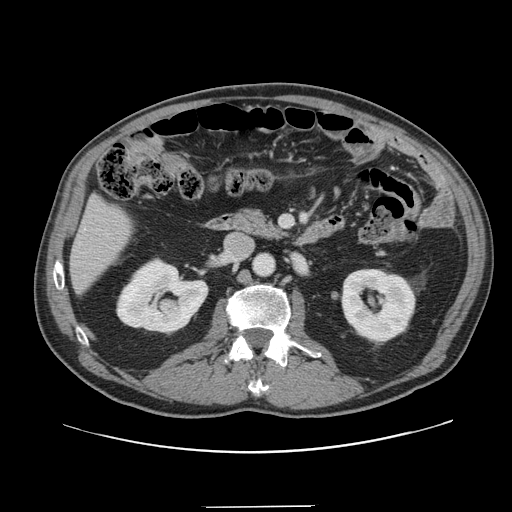
Contrast-enhanced abdominal CT, one axial slice; position 58 of 139 along the scan axis; 120 kVp; intravenous contrast given; soft-tissue window (W 400 / L 40 HU); 2.5 mm slice thickness; 512 × 512 image matrix, field of view 397 × 397 mm. Male patient, age 64 years. Case-level facts recorded for this patient, not image findings: diagnosis: colorectal cancer liver metastases, imaged before liver resection; multiple liver metastases: yes; largest metastasis: 3.5 cm; chemotherapy before resection: yes.
Outlined on this slice (manually delineated by an expert):
- liver: bounding box (x1, y1, x2, y2) in pixels: (71, 199, 132, 290)
- planned liver remnant (the part of the liver to remain after resection): (71, 199, 134, 289)